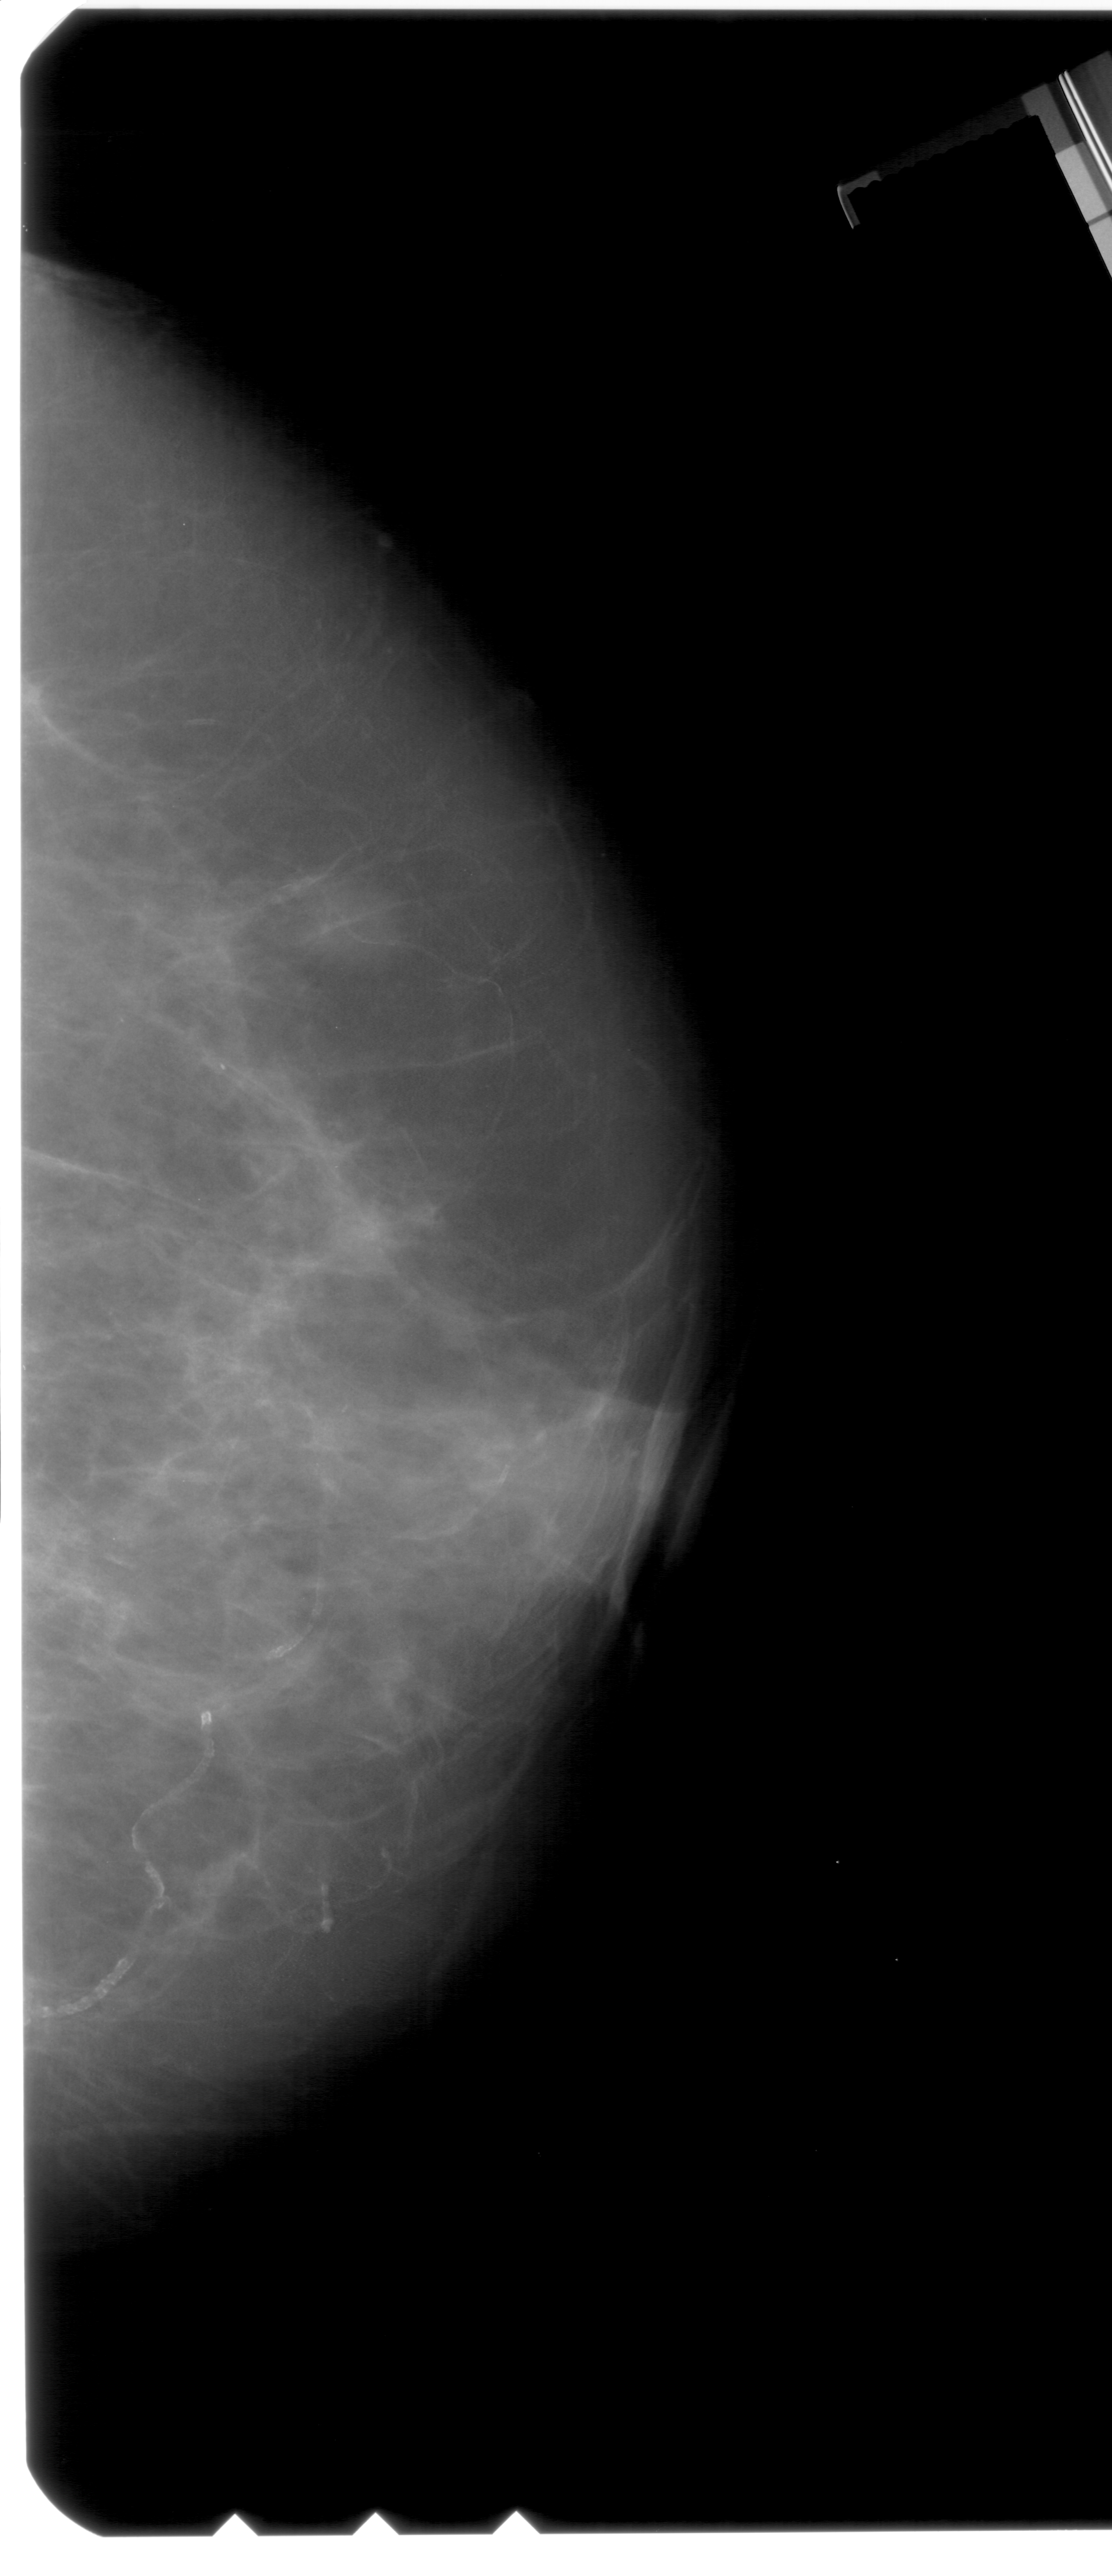
Scanned film-screen mammogram. Right breast. Craniocaudal (CC) view. Breast composition: extremely dense (BI-RADS density category 4 of 4). 1112 × 2576 image matrix.
Expert-marked regions of interest on this image (one box per marked abnormality):
- mass, shape oval, margins ill defined; BI-RADS assessment category 4; pathology (as recorded): benign: bounding box (x1, y1, x2, y2) in pixels: (225, 859, 421, 996)